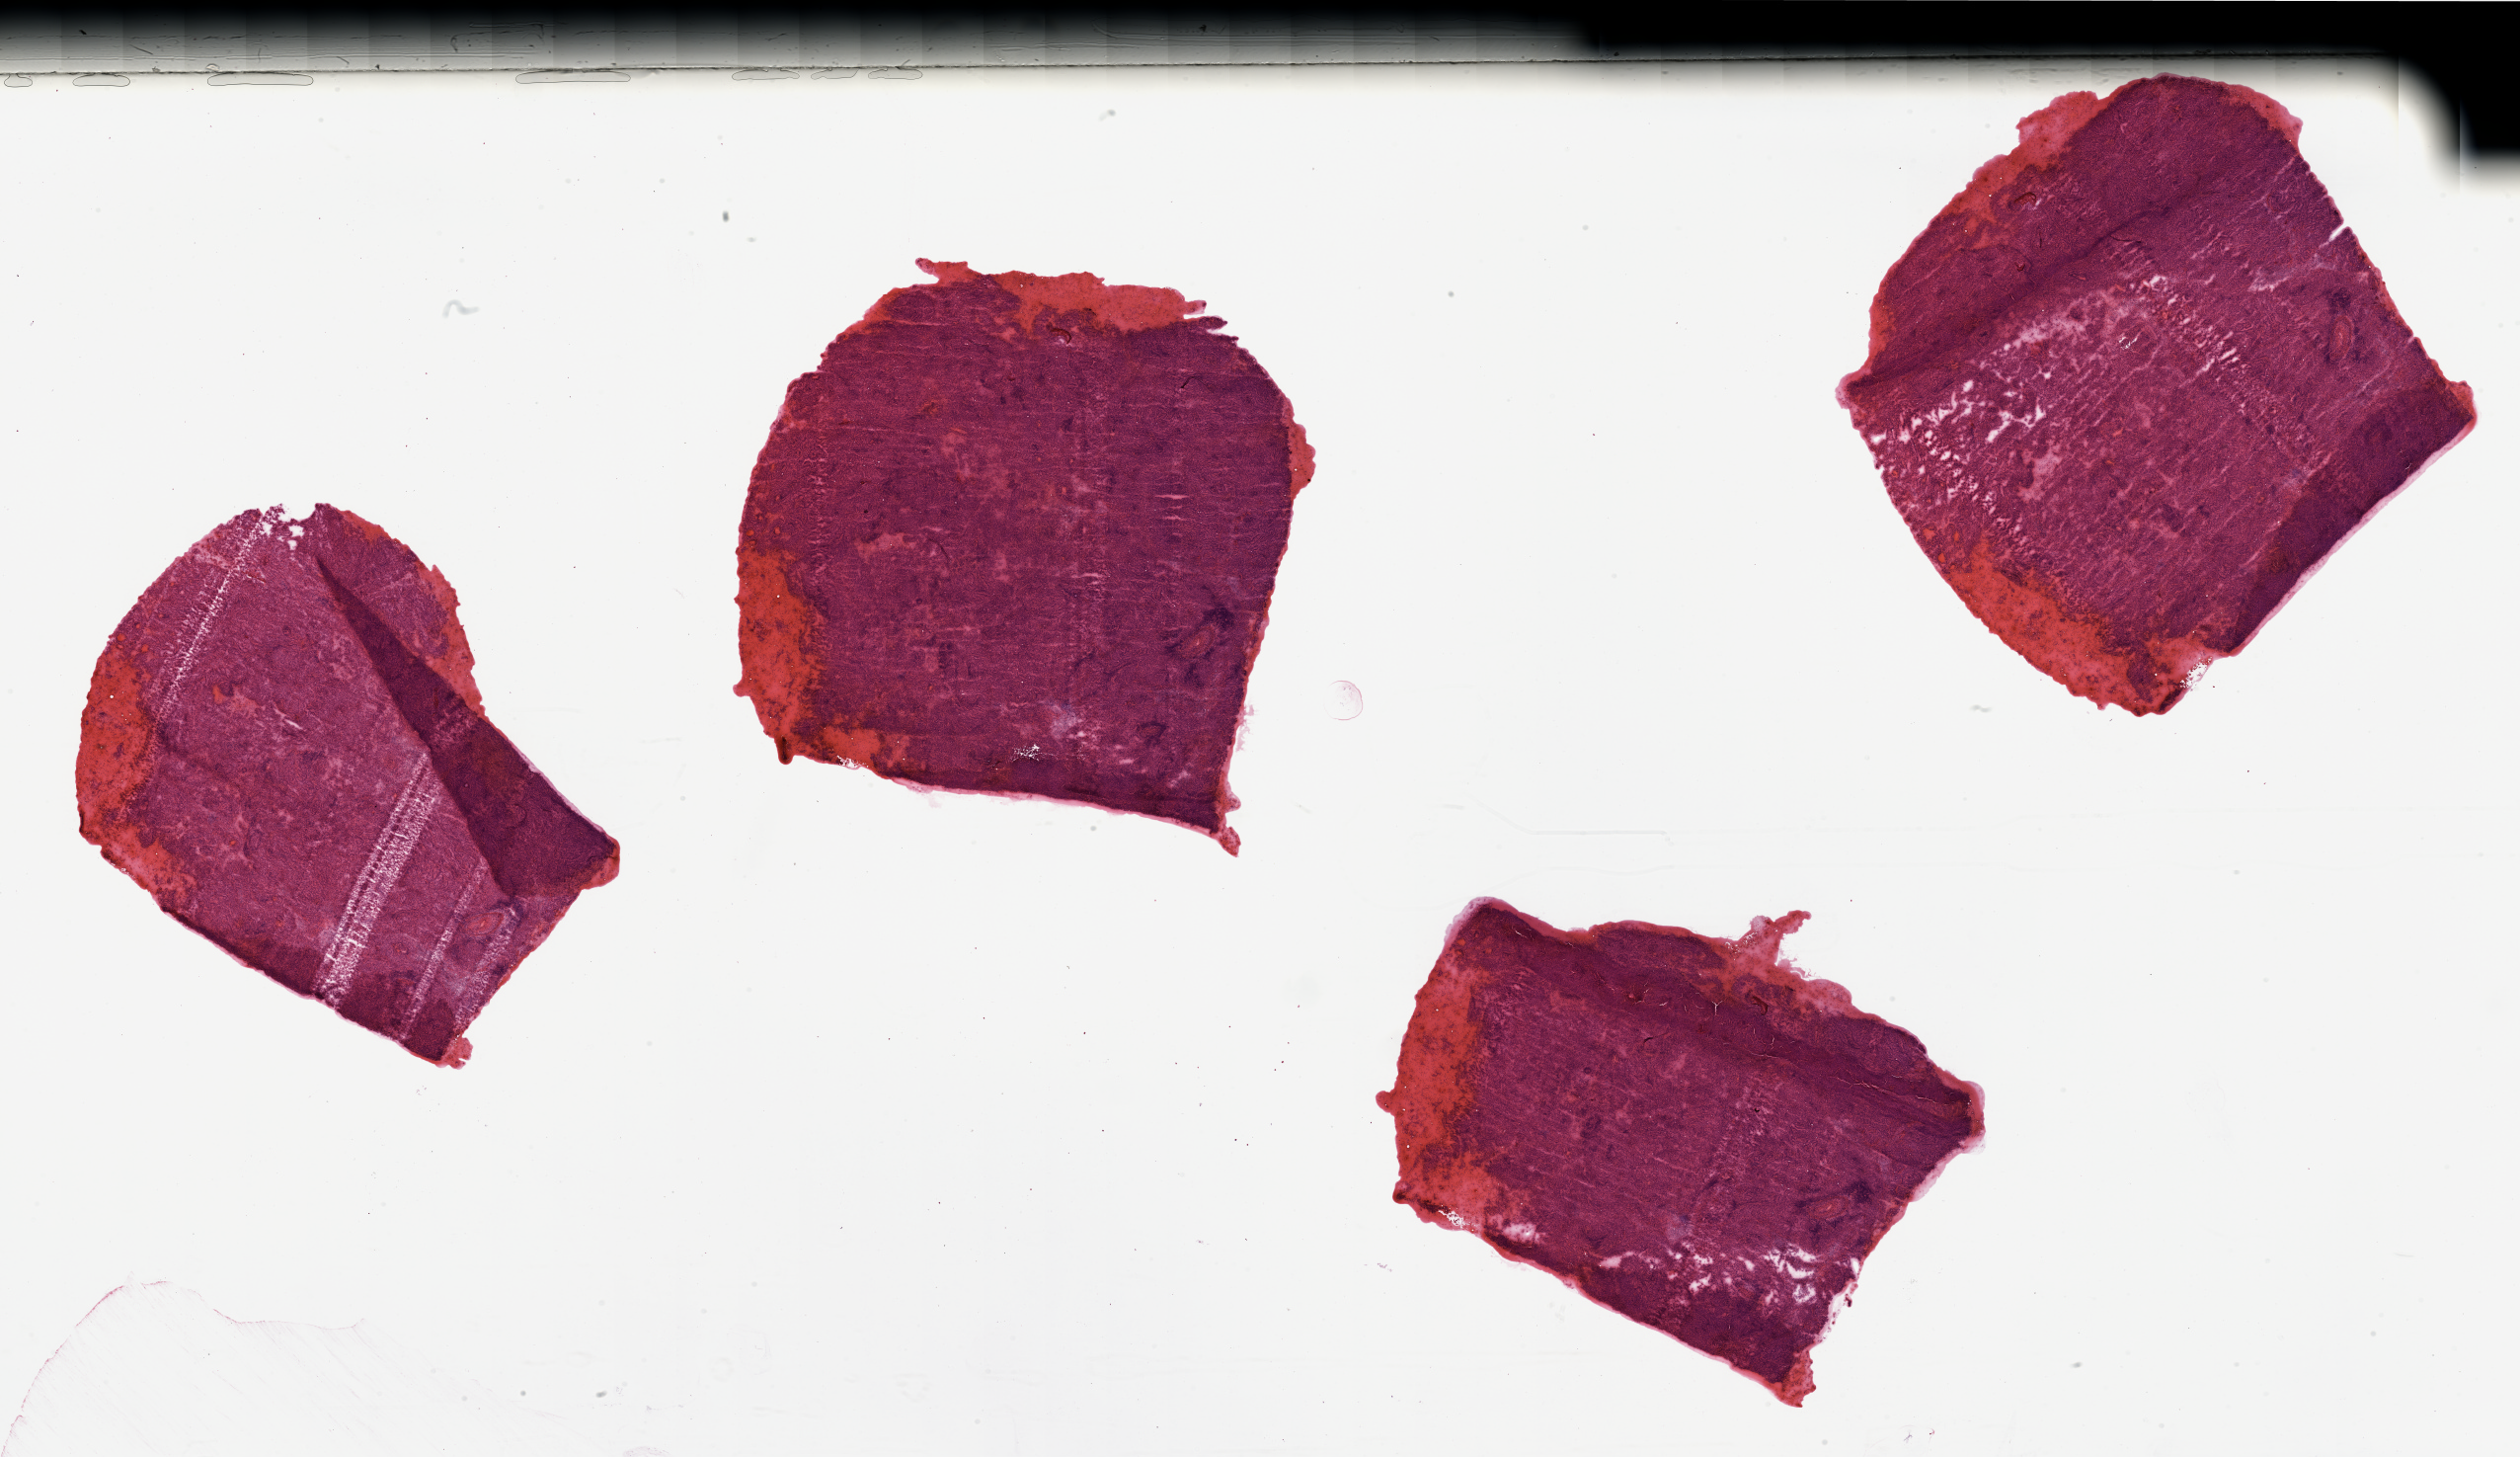
Whole-slide histology image, Hematoxylin and eosin (H&E) stained, shown as a low-resolution overview of the whole scanned area (about 40.4 x 23.3 mm), lung, tumour tissue. Patient: male, age 57 years. Histologic grade: GX (grade cannot be assessed).
- AJCC pathologic stage: IIB
- histologic diagnosis: Adenocarcinoma, NOS
- primary tumour site (as recorded): right lower lobe